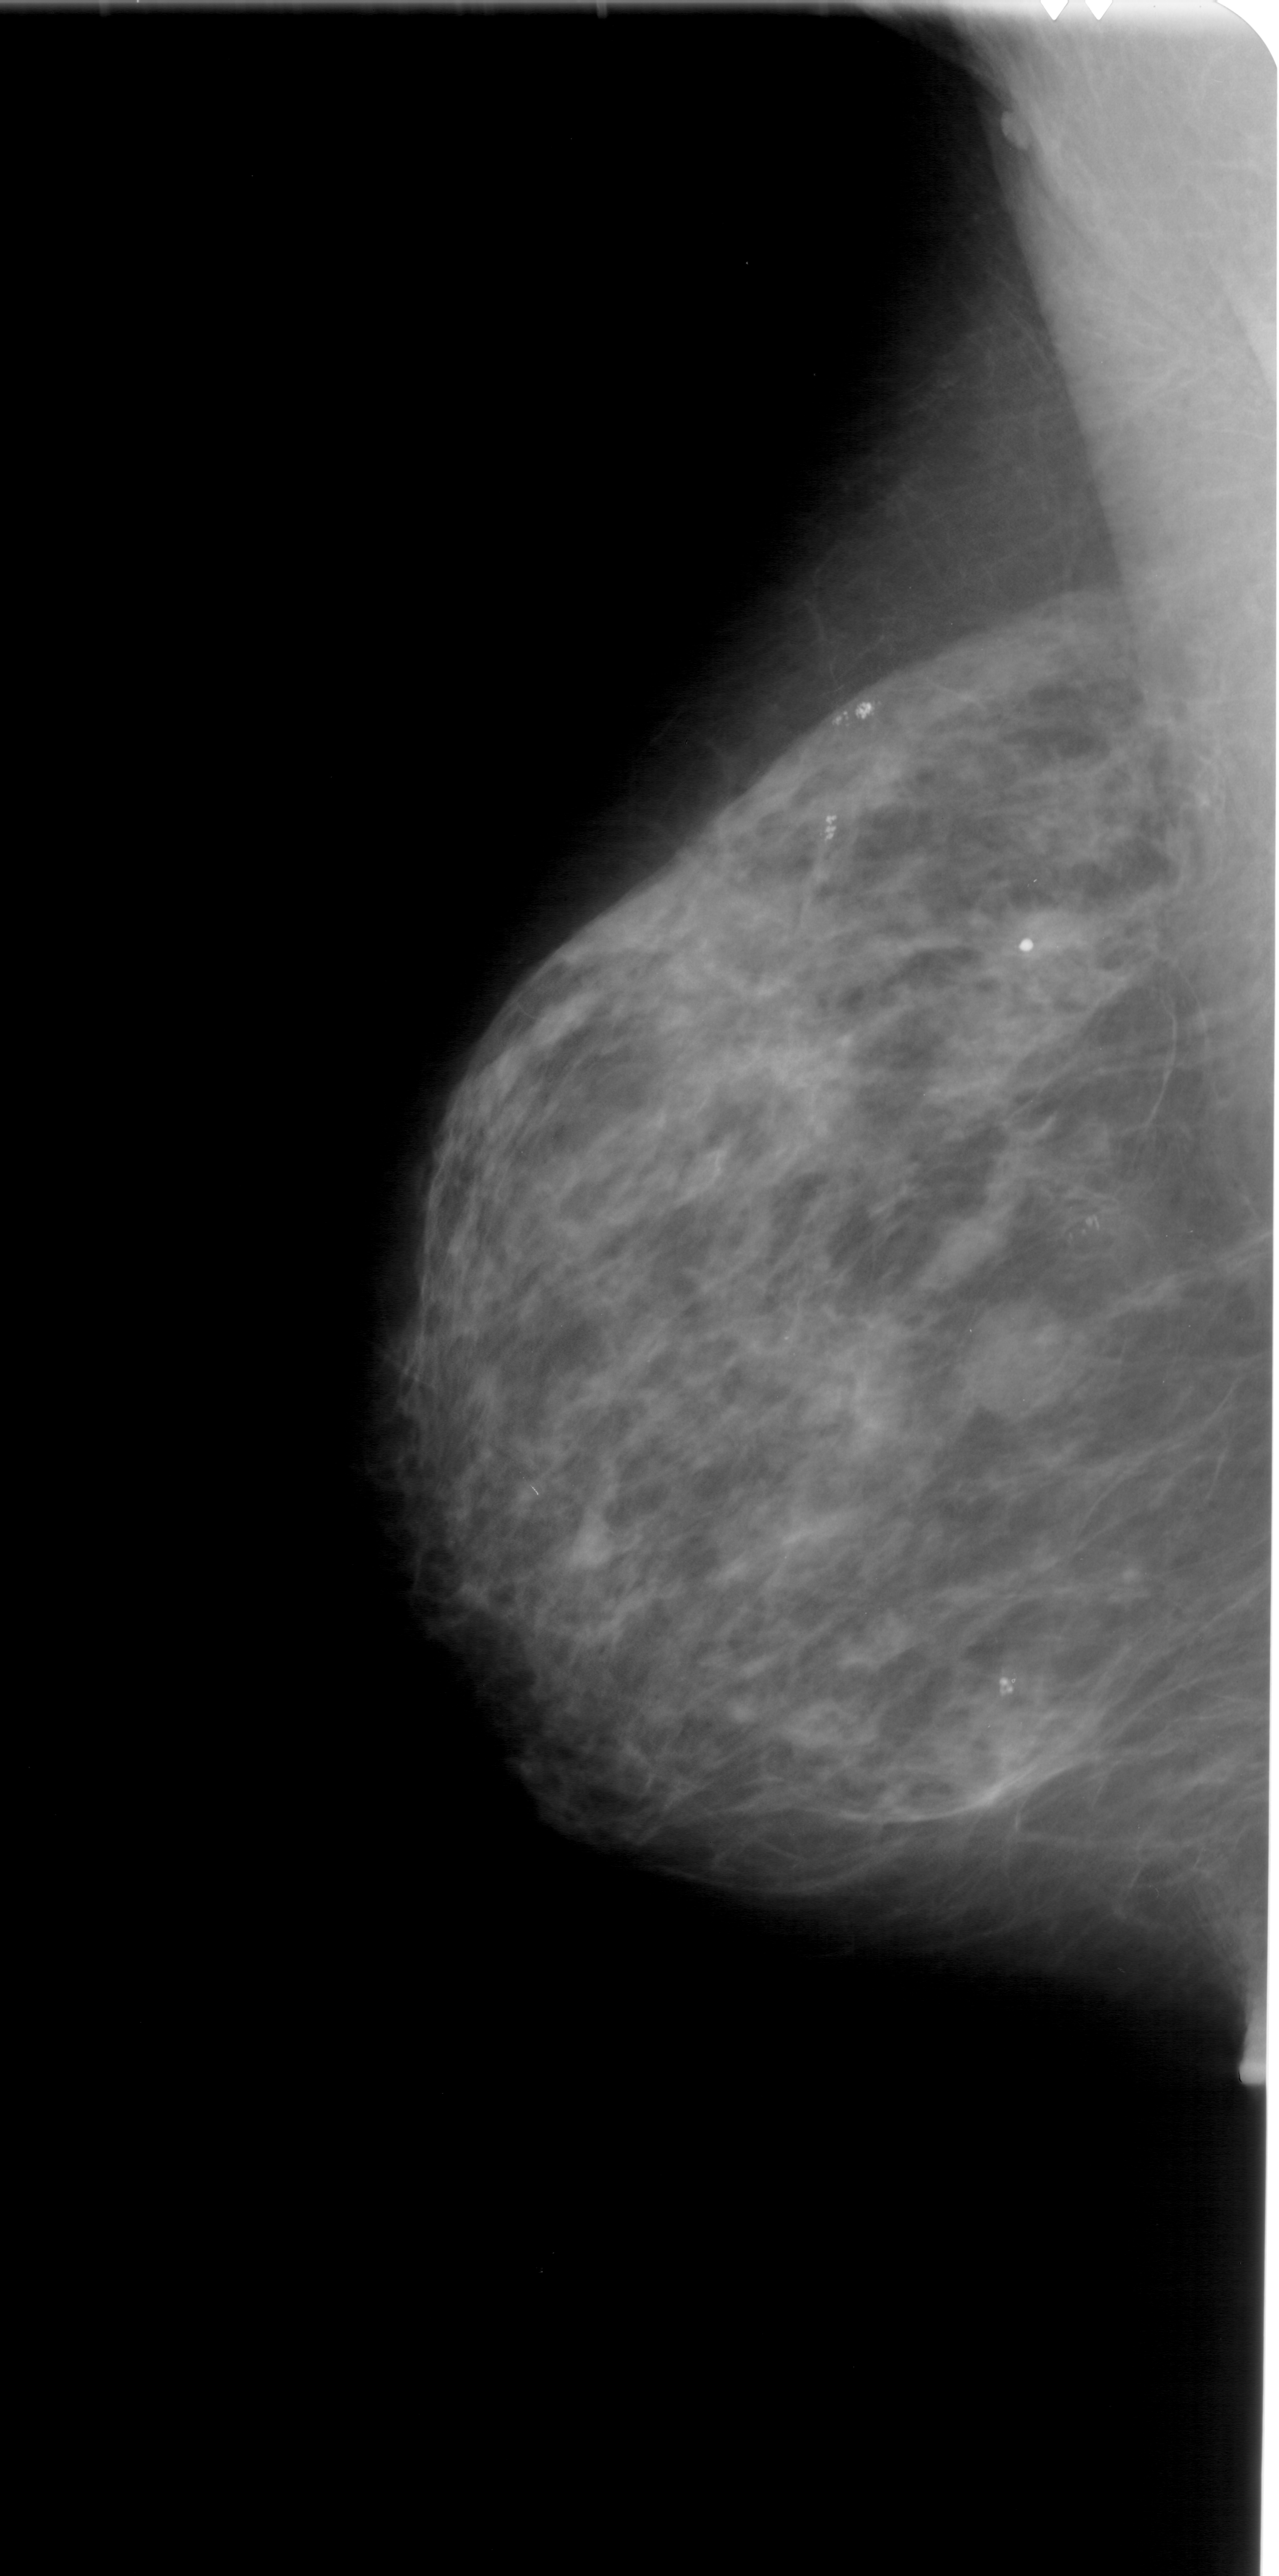
Mammogram (digitized film). Left breast. MLO view. Breast composition: heterogeneously dense (BI-RADS density category 3 of 4). 1279 × 2576 image matrix.
Expert-marked regions of interest on this film, with their recorded descriptors:
- mass, shape lobulated, margins ill defined; BI-RADS assessment category 4; pathology result (as recorded, not read from the image): benign: bounding box (x1, y1, x2, y2) in pixels: (951, 1286, 1081, 1420)